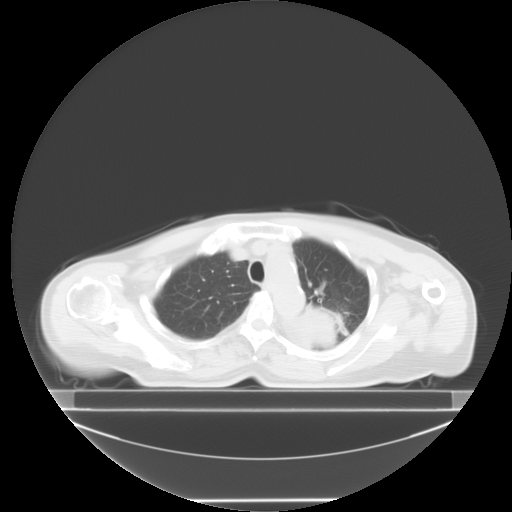
Chest CT, one axial slice; slice 12 of 24 in the series (ordered by position); reconstruction kernel STANDARD; lung window (W 1500 / L -600 HU); 5 mm slice thickness; 512 × 512 image matrix, field of view 500 × 500 mm. Female patient, age 74 years. Case-level facts recorded for this patient, not image findings: clinical TNM (as recorded): T3 N1 M1c; histopathological grade: G3.
Outlined on this slice (bounding box drawn by a radiologist):
- lung tumour (recorded histology: small cell carcinoma): bounding box <277,297,337,353> (left, top, right, bottom; pixels)